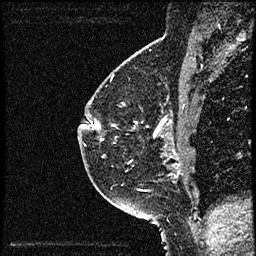
Breast MRI (dynamic contrast-enhanced), one sagittal slice; slice 38 of 52 in the series (ordered by position); dynamic contrast-enhanced study with each time point stored as its own series, time point 2 of 3 at this slice position (early post-contrast, ordered by acquisition time); 1.5 T; TE 4.2 ms, TR 17.6 ms; 2 mm slice thickness; 256 × 256 image matrix, field of view 200 × 200 mm. Patient: female, 49 years. From the clinical record (not read from this slice): setting: breast cancer imaged before/during neoadjuvant chemotherapy; receptor status: HER2-positive.
Annotated regions visible in this slice (semi-automatic segmentation, software-assisted and operator-edited):
- analysis volume of interest (the breast-tissue region the enhancement analysis was run in; not a lesion): bounding box (x1, y1, x2, y2) in pixels: (85, 65, 182, 175)
- tumour enhancement mask (voxels above the 100 % enhancement threshold inside the analysis volume of interest): (92, 122, 179, 160)